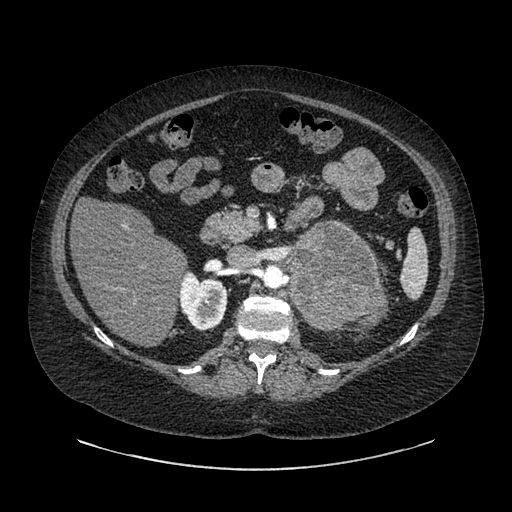
Contrast-enhanced abdominal CT, one axial slice; position 540 of 769 along the scan axis; reconstruction kernel SOFT; intravenous contrast given; soft-tissue window (W 400 / L 40 HU); 512 × 512 image matrix, field of view 460 × 460 mm. Patient: female, 61 years. Case-level facts recorded for this patient, not image findings: diagnosis: adrenocortical carcinoma; tumour side: left adrenal; tumour size at pathology: 13 cm; Ki-67 index: 79 %; stage (as recorded): 2.
Structures marked on this image (semi-automatic segmentation, software-assisted and operator-edited):
- mass: bounding box <289,225,376,328> (left, top, right, bottom; pixels)